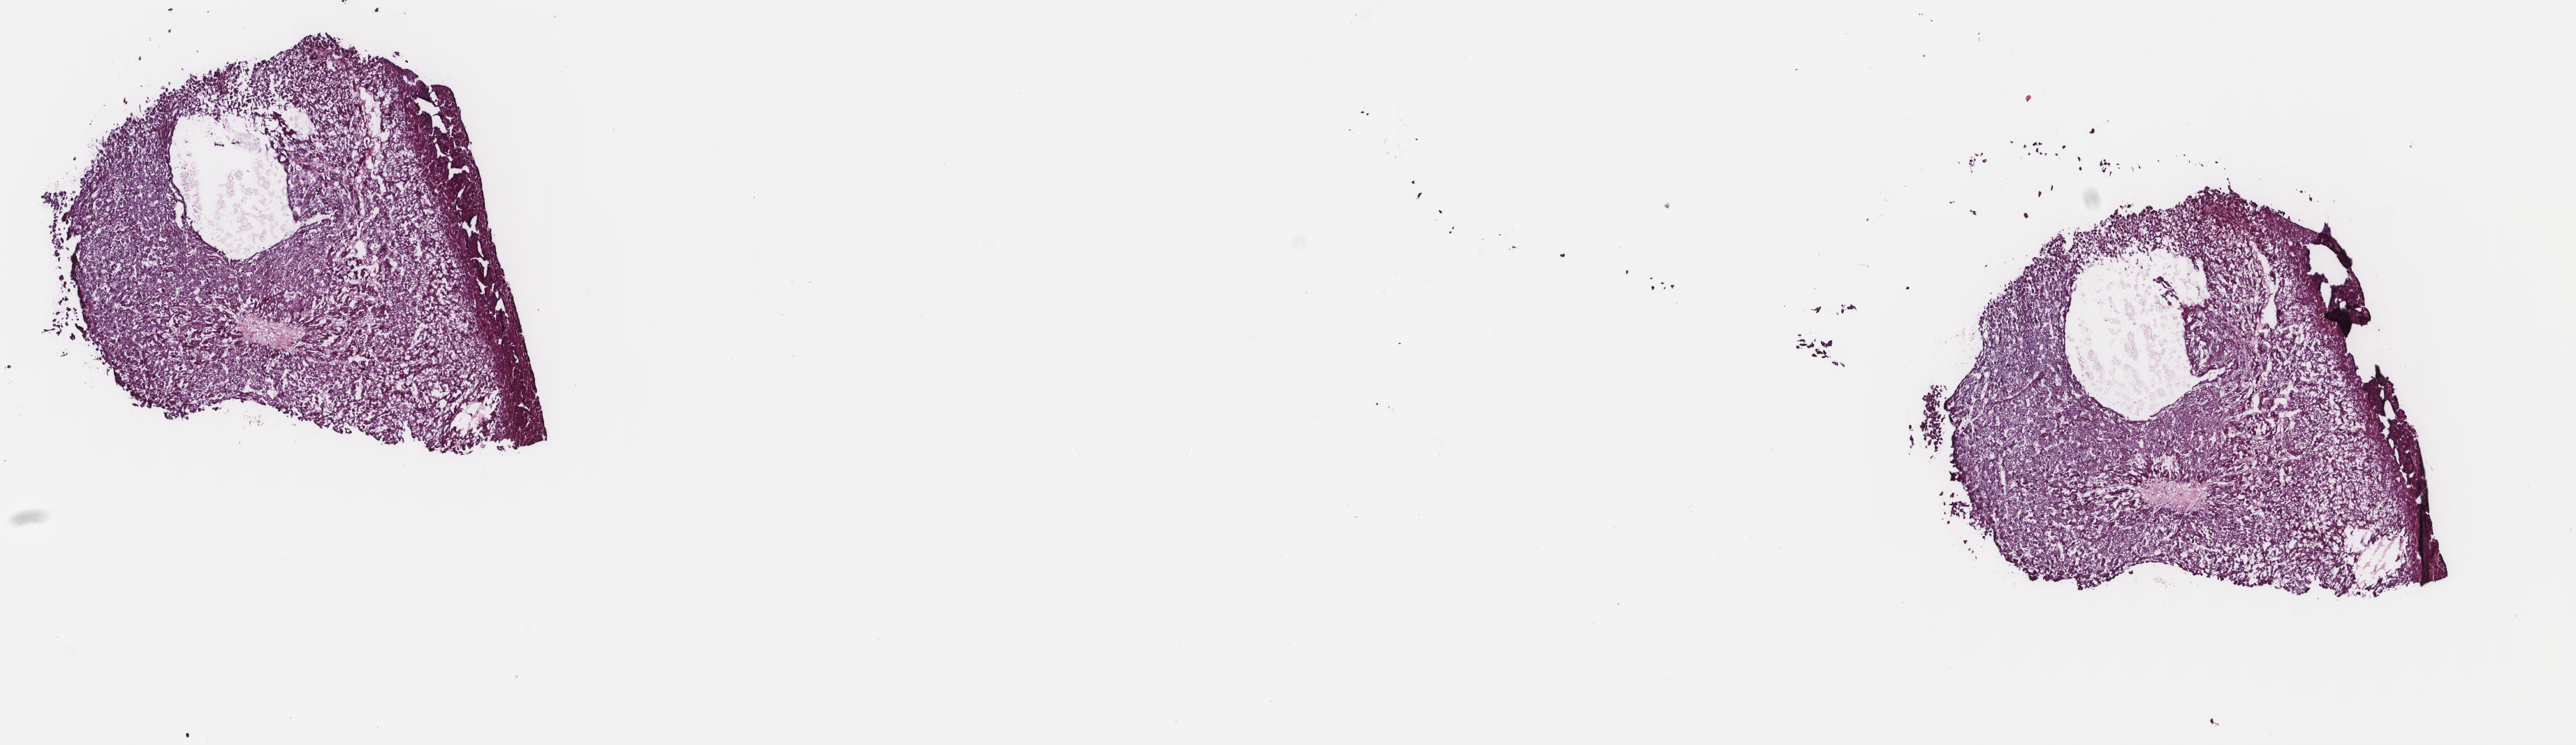
Whole-slide histology image, H&E-stained — whole scanned area (about 14.6 x 4.2 mm, slide scanned at 40x) shown as a low-resolution overview; frozen section; sample: primary tumour, liver. Male, age 37 years at initial diagnosis.
Pathologic diagnosis: Hepatocellular carcinoma, NOS.